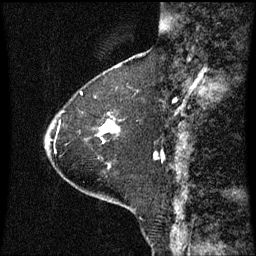
Breast MRI (dynamic contrast-enhanced), one sagittal slice. Slice 21 of 60 in the series (ordered by position). Dynamic contrast-enhanced series, image 2 of 3 at this slice position (ordered by acquisition). 1.5 T. TE 4.2 ms, TR 8.9 ms. 256 × 256 image matrix, field of view 200 × 200 mm. Female patient, age 63 years. From the clinical record (not read from this slice): setting: breast cancer imaged before/during neoadjuvant chemotherapy; receptor status: HR-positive, HER2-negative.
Structures marked on this image (semi-automatic segmentation, software-assisted and operator-edited):
- analysis volume of interest (the breast-tissue region the enhancement analysis was run in; not a lesion): bounding box [x1, y1, x2, y2] px = [98, 122, 116, 143]
- tumour enhancement mask (voxels above the 70 % enhancement threshold inside the analysis volume of interest): [101, 122, 116, 135]